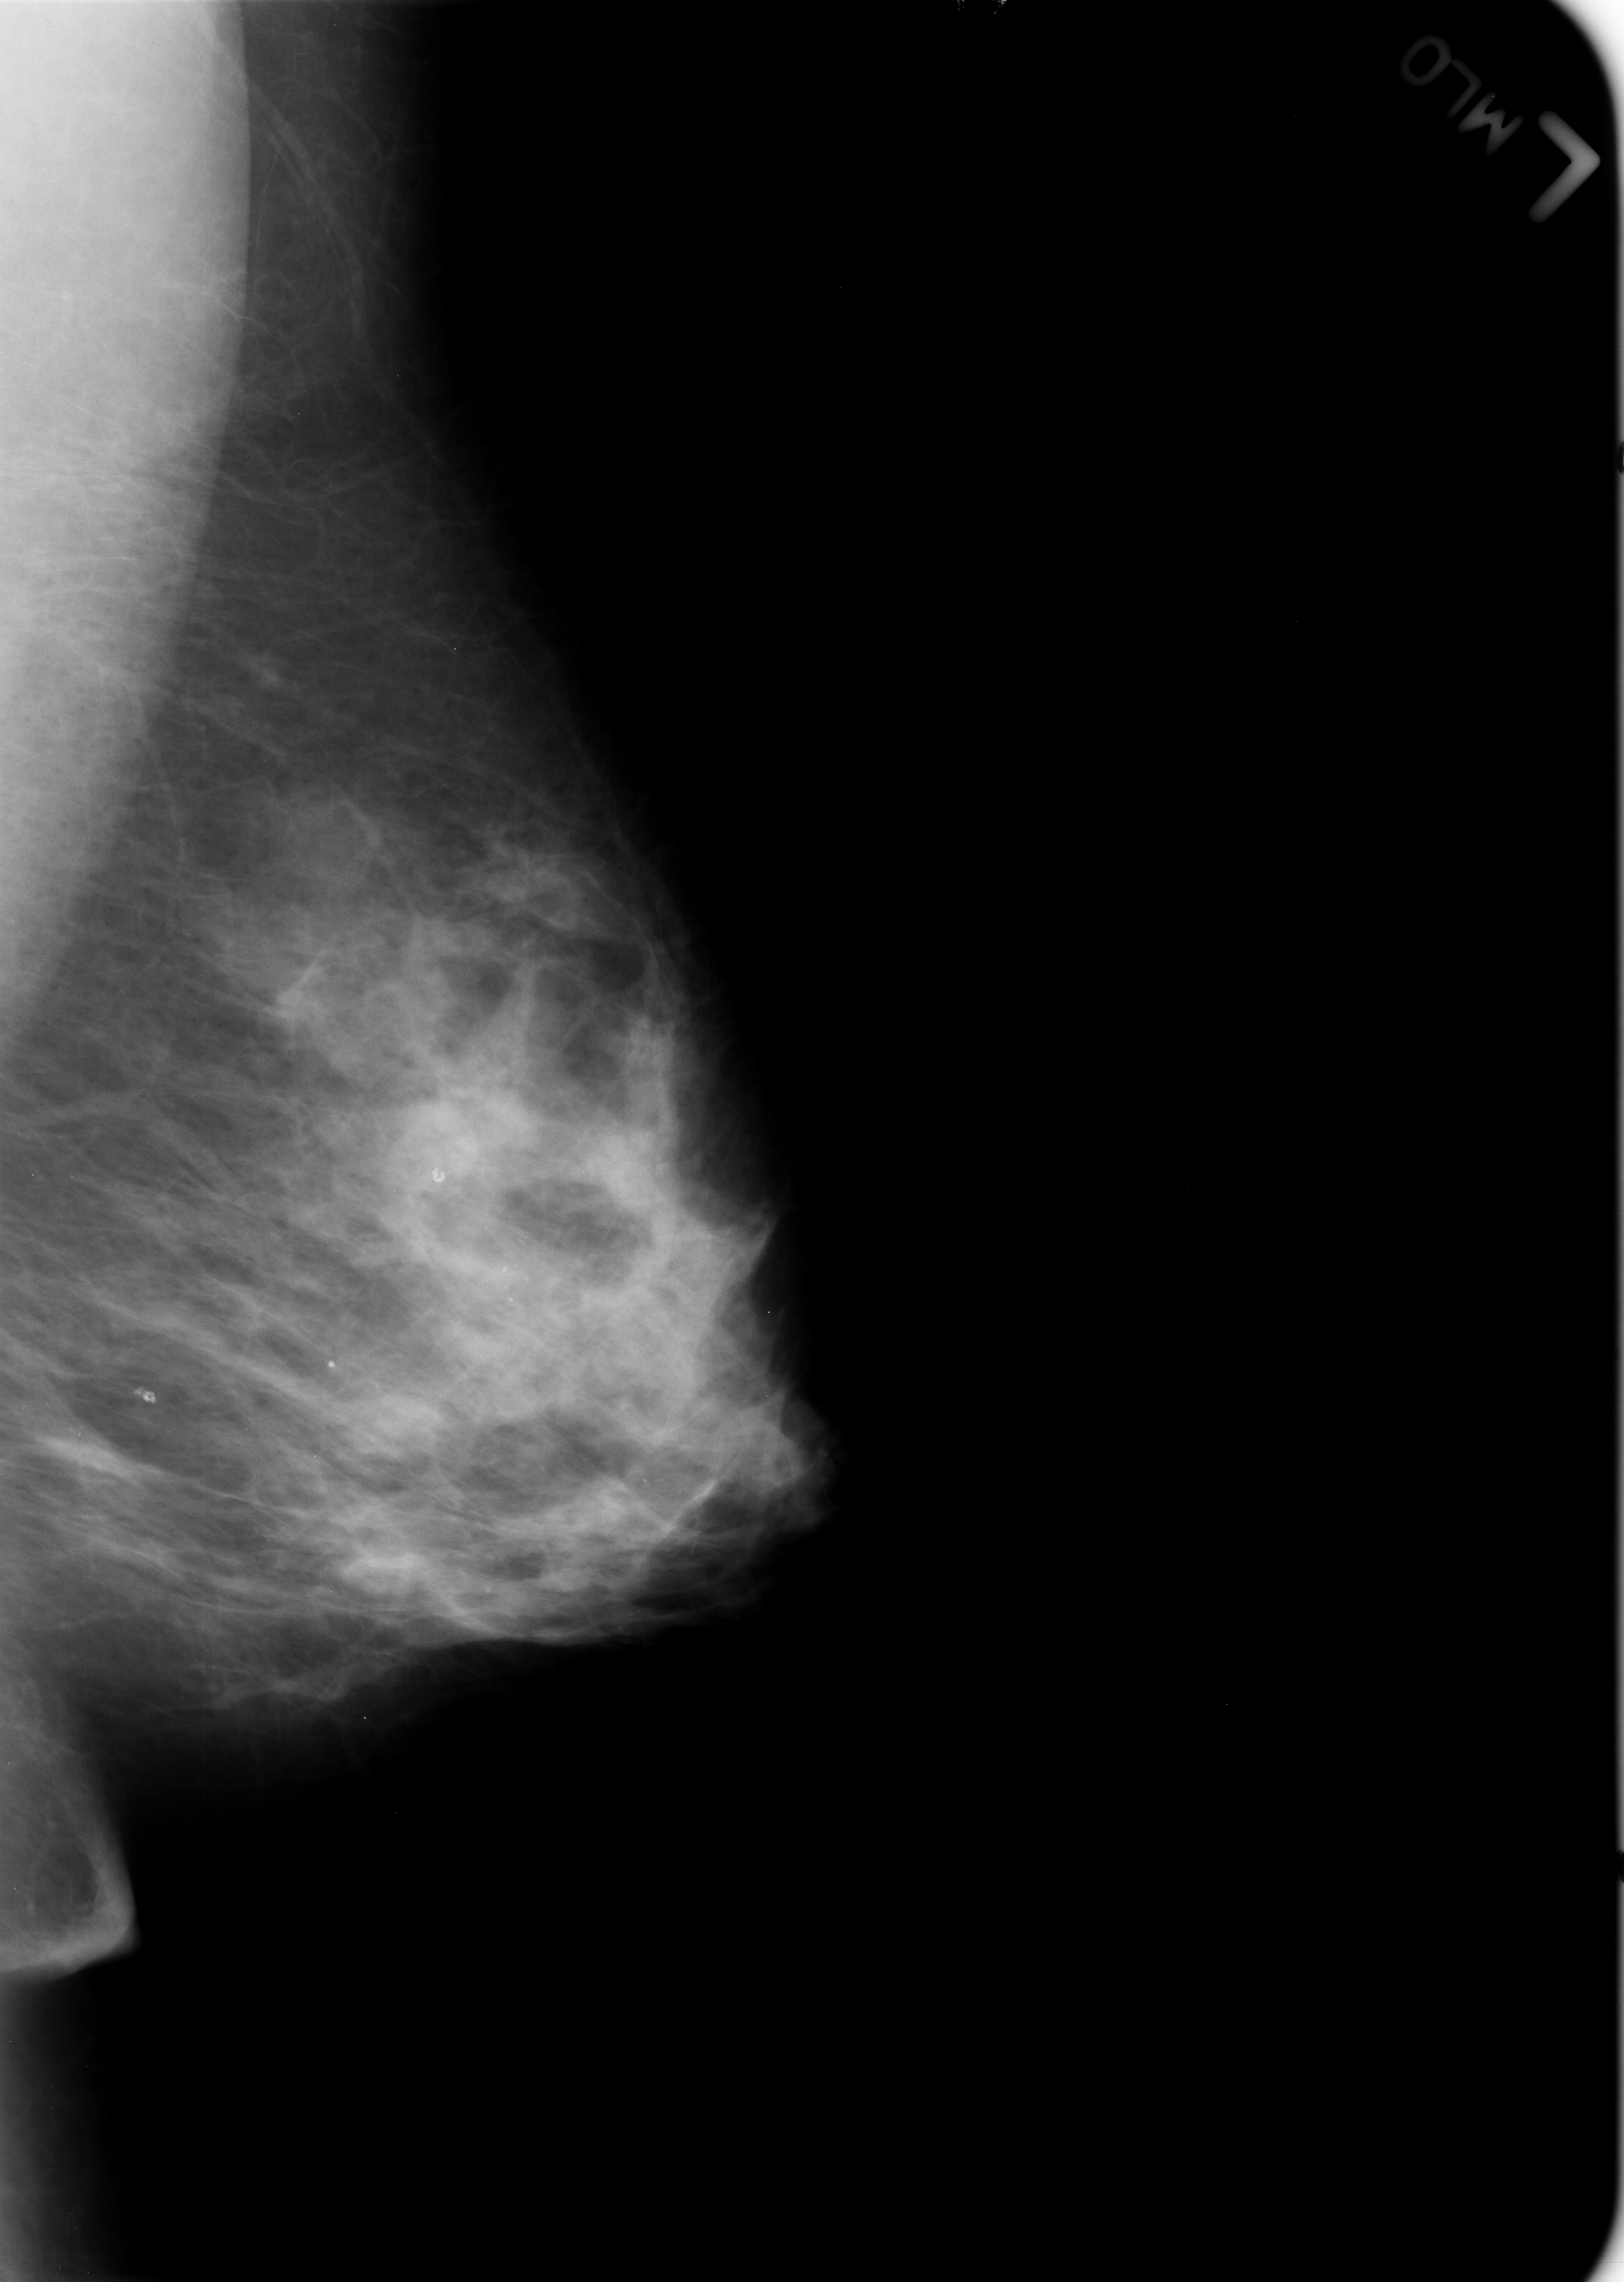
Mammogram (digitized film); left breast; mediolateral oblique (MLO) view; breast composition: heterogeneously dense (BI-RADS density category 3 of 4); 1624 × 2282 image matrix.
Marked abnormalities (boxes around the expert regions of interest):
- Finding 1 of 3: calcifications, morphology round and regular / lucent center; BI-RADS assessment category 2; subtlety rating 5 on a 1 (subtle) to 5 (obvious) scale; outcome (as recorded, no biopsy): benign without callback (not worked up further): bounding box (x1, y1, x2, y2) in pixels: (119, 1369, 181, 1432)
- Finding 2 of 3: calcifications, morphology round and regular / lucent center; BI-RADS assessment category 2; subtlety rating 5 on a 1 (subtle) to 5 (obvious) scale; outcome (as recorded, no biopsy): benign without callback (not worked up further): (302, 1340, 368, 1403)
- Finding 3 of 3: calcifications, morphology round and regular / lucent center; BI-RADS assessment category 2; benign; no additional work-up was recommended (outcome (as recorded, no biopsy): benign without callback): (396, 1153, 487, 1222)